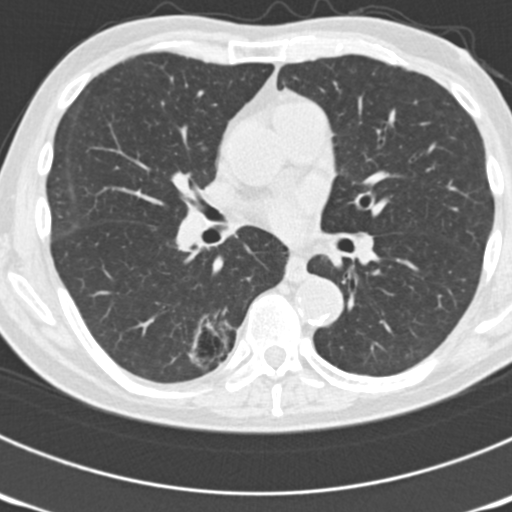
Low-dose screening chest CT, axial slice; third annual screen; lung window (W 1500 / L -600 HU); 2 mm slice thickness; standard (soft-tissue) reconstruction kernel (B30f); 120 kVp; 512 × 512 image matrix. Male, age 70 years at enrolment. Current smoker at enrolment.
Expert reader's lesion annotation, bounding box <147,304,238,385> (left, top, right, bottom; pixels). The screening reader recorded 3 non-calcified nodules or masses ≥4 mm on this exam; which of them this box marks is not recorded. Participant outcome: lung cancer diagnosed 14 days after this screen — bronchiolo-alveolar adenocarcinoma, NOS, right lower lobe, poorly differentiated (G3), stage IB (AJCC 6th edition), 30 mm at pathology.